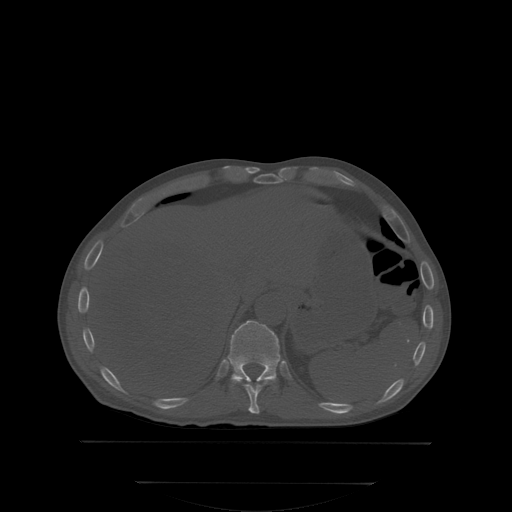
CT including the spine, one axial slice; slice 186 of 350 in the series (ordered by position); bone window (W 1800 / L 400 HU); 512 × 512 image matrix, field of view 500 × 500 mm. Patient: male, 58 years. Case-level facts recorded for this patient, not image findings: primary cancer: prostate; vertebrae with lytic lesions (as recorded): L1.
Outlined on this slice (semi-automatically segmented with operator editing):
- T10 vertebra: bounding box (x1, y1, x2, y2) in pixels: (234, 379, 274, 413)
- T11 vertebra: (228, 320, 280, 382)